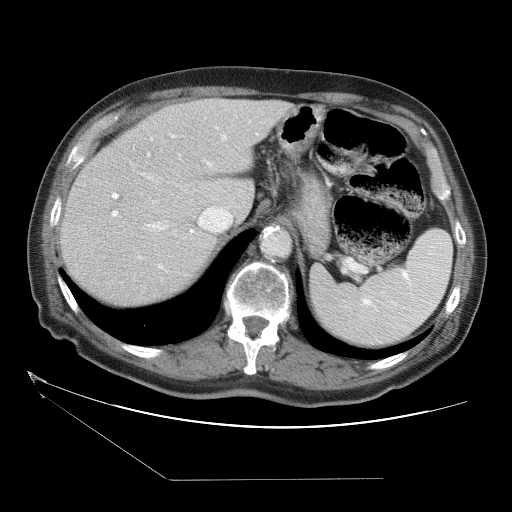
Contrast-enhanced abdominal CT (liver protocol), one axial slice; position 25 of 38 along the scan axis; 120 kVp; one of 2 acquisitions stored at this slice position; soft-tissue window (W 400 / L 40 HU); 512 × 512 image matrix, field of view 400 × 400 mm. Case-level facts recorded for this patient, not image findings: diagnosis: hepatocellular carcinoma (patient treated with transarterial chemoembolisation; whether this scan precedes or follows treatment is not stated here); TNM stage (as recorded): Stage-II; Child-Pugh class: A; tumour differentiation: moderately differentiated; tumour nodularity: multinodular.
Outlined on this slice (semi-automatically segmented with operator editing):
- abdominal aorta: bounding box [x1, y1, x2, y2] px = [263, 231, 291, 258]
- liver parenchyma outside the tumour (the mass and vessels are separate outlines, so this box may not span the whole liver): [59, 98, 296, 304]
- liver vessels: [111, 134, 227, 289]